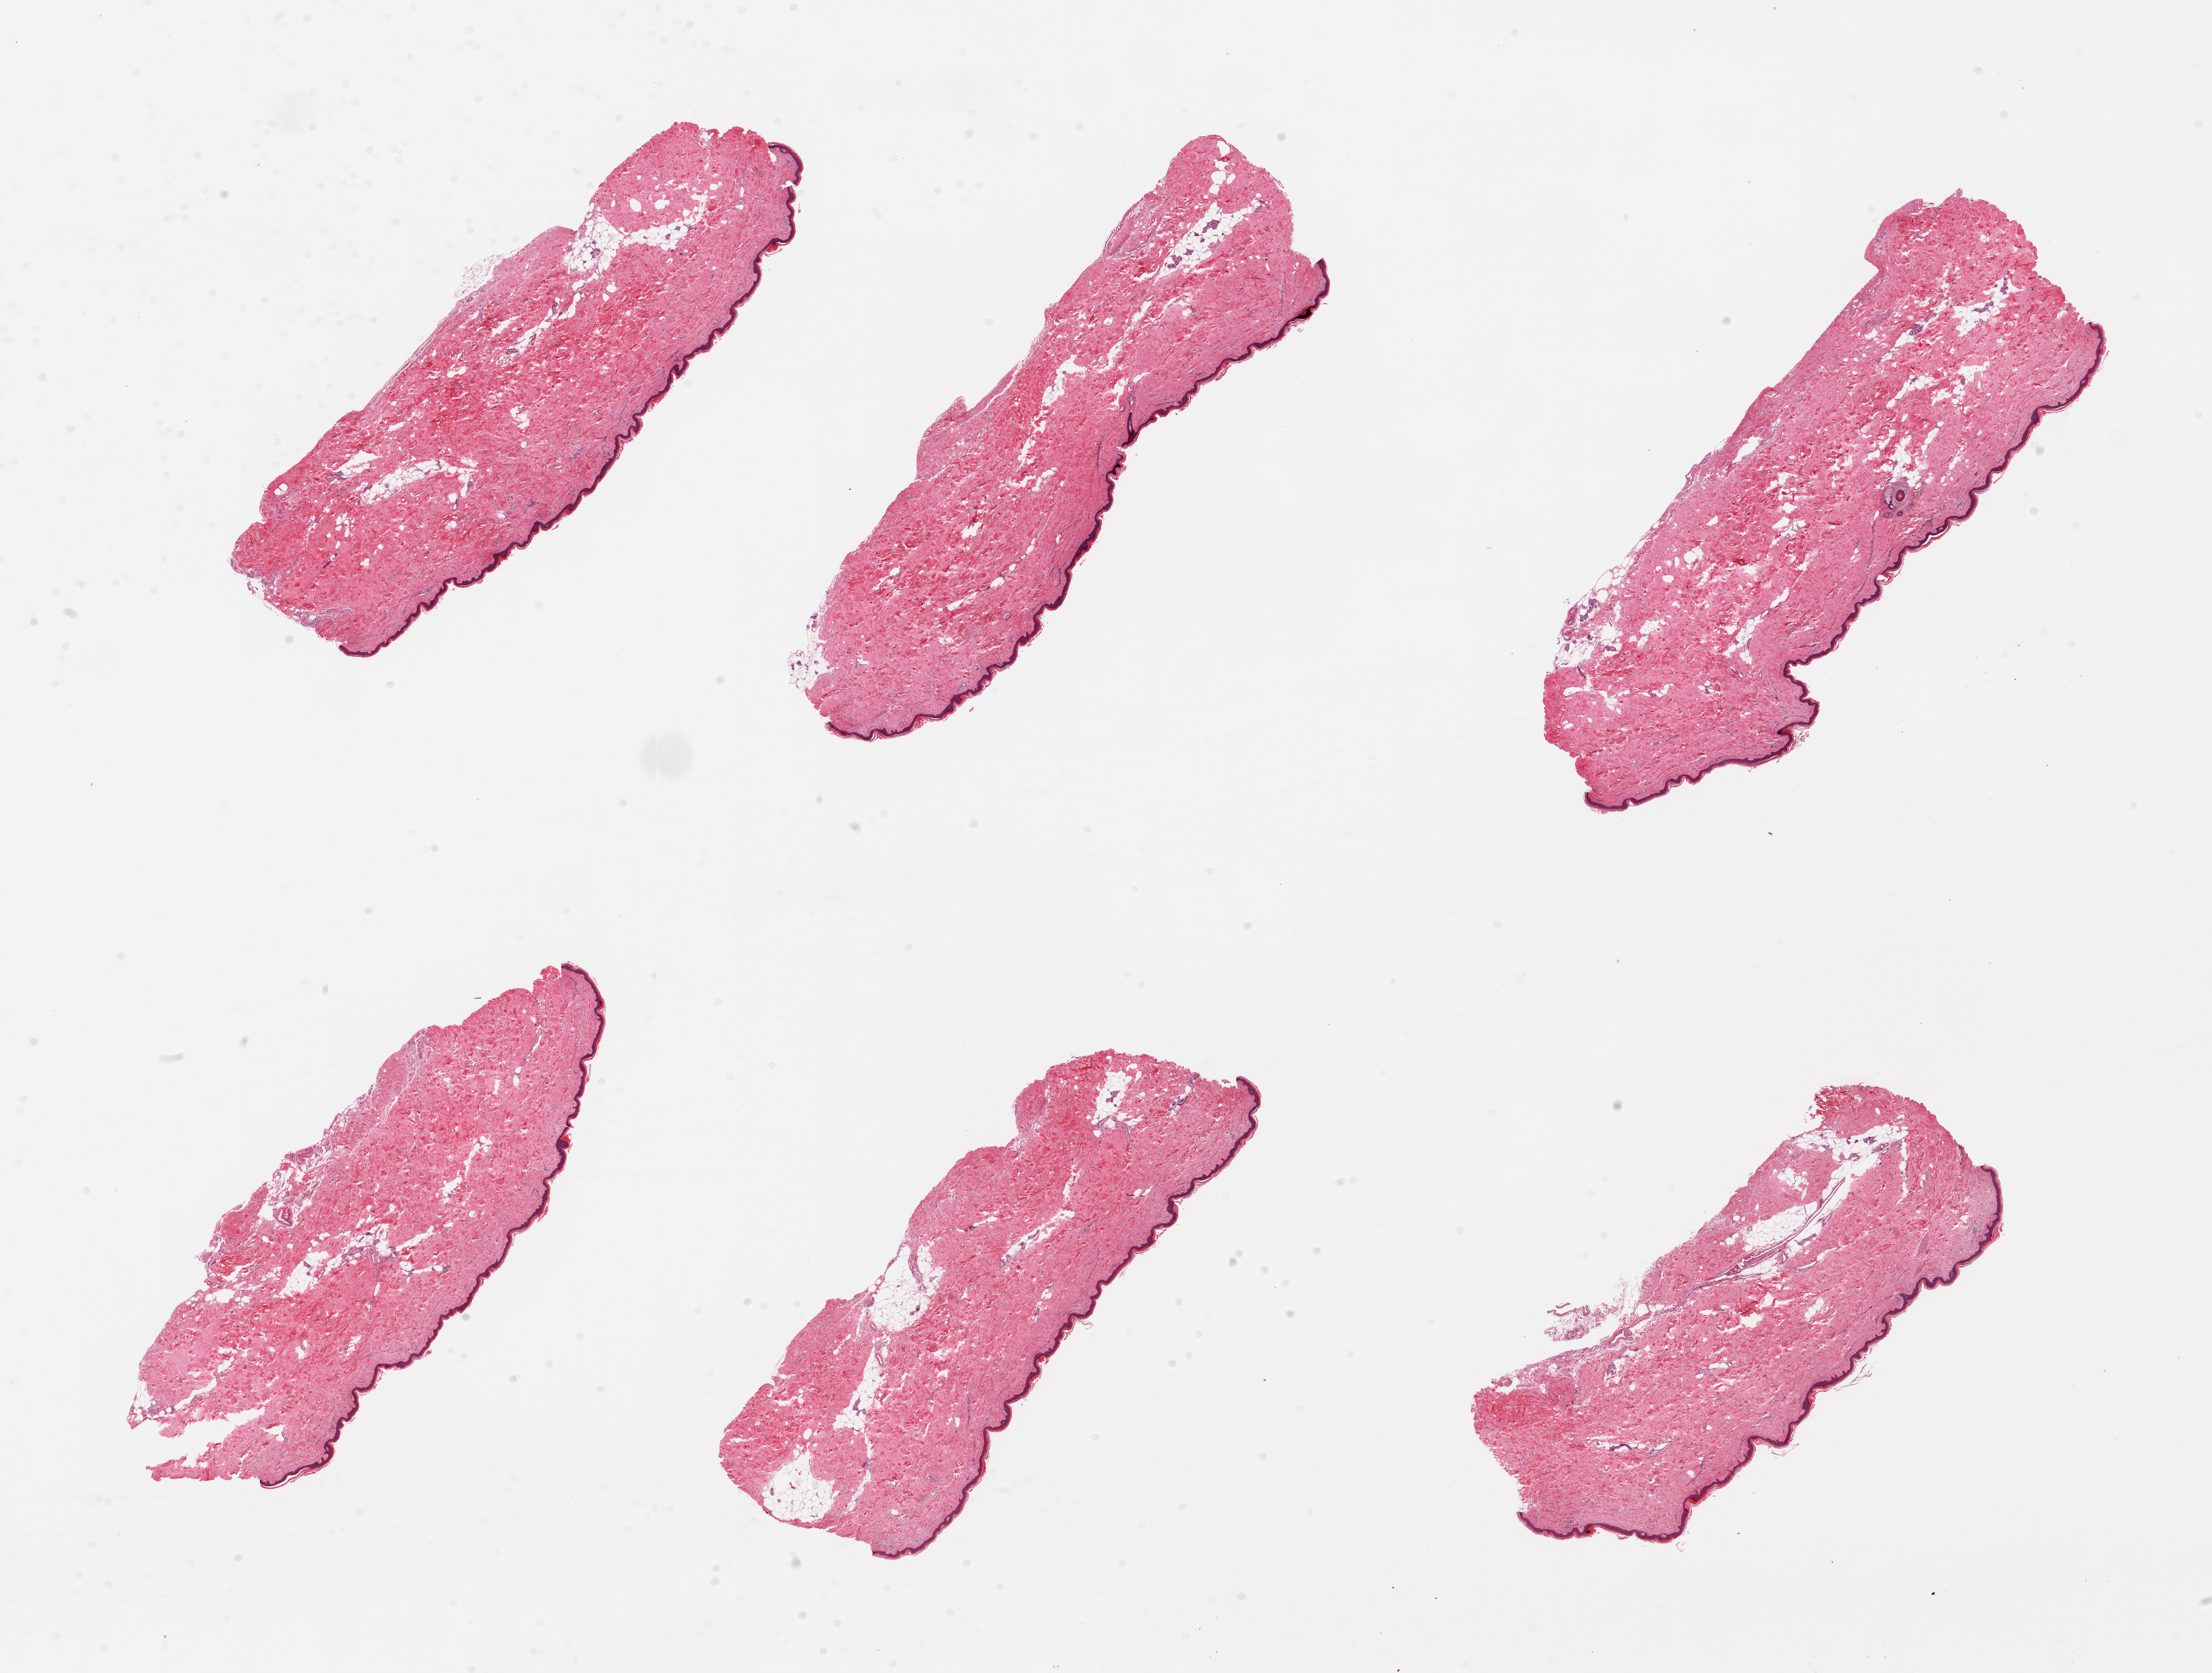
Whole-slide image, haematoxylin and eosin stain, brightfield, shown as a low-resolution overview of the whole scanned area (about 26.6 x 20.1 mm), PAXgene-fixed paraffin-embedded (PFPE) section, sampled site (target tissue): skin of lower leg, tissue donor sample. Female donor.
Reviewer comment on this tissue sample: 6 pieces; ~10% internal fat, epidermis measures 31 microns.